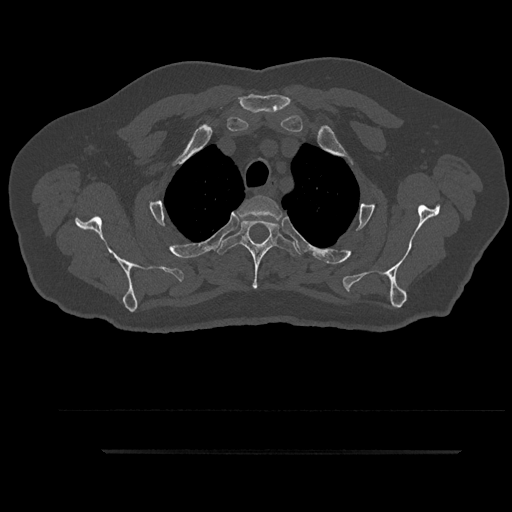
CT including the spine, one axial slice; position 727 of 797 along the scan axis; reconstruction kernel Br40s/3; bone window (W 1800 / L 400 HU); 512 × 512 image matrix. Male patient, age 63 years. From the clinical record (not read from this slice): primary cancer: renal.
Annotated regions visible in this slice (semi-automatically segmented with operator editing):
- T2 vertebra: box from (x=238, y=195) to (x=283, y=221) px
- T3 vertebra: (x=215, y=219)–(x=301, y=289)